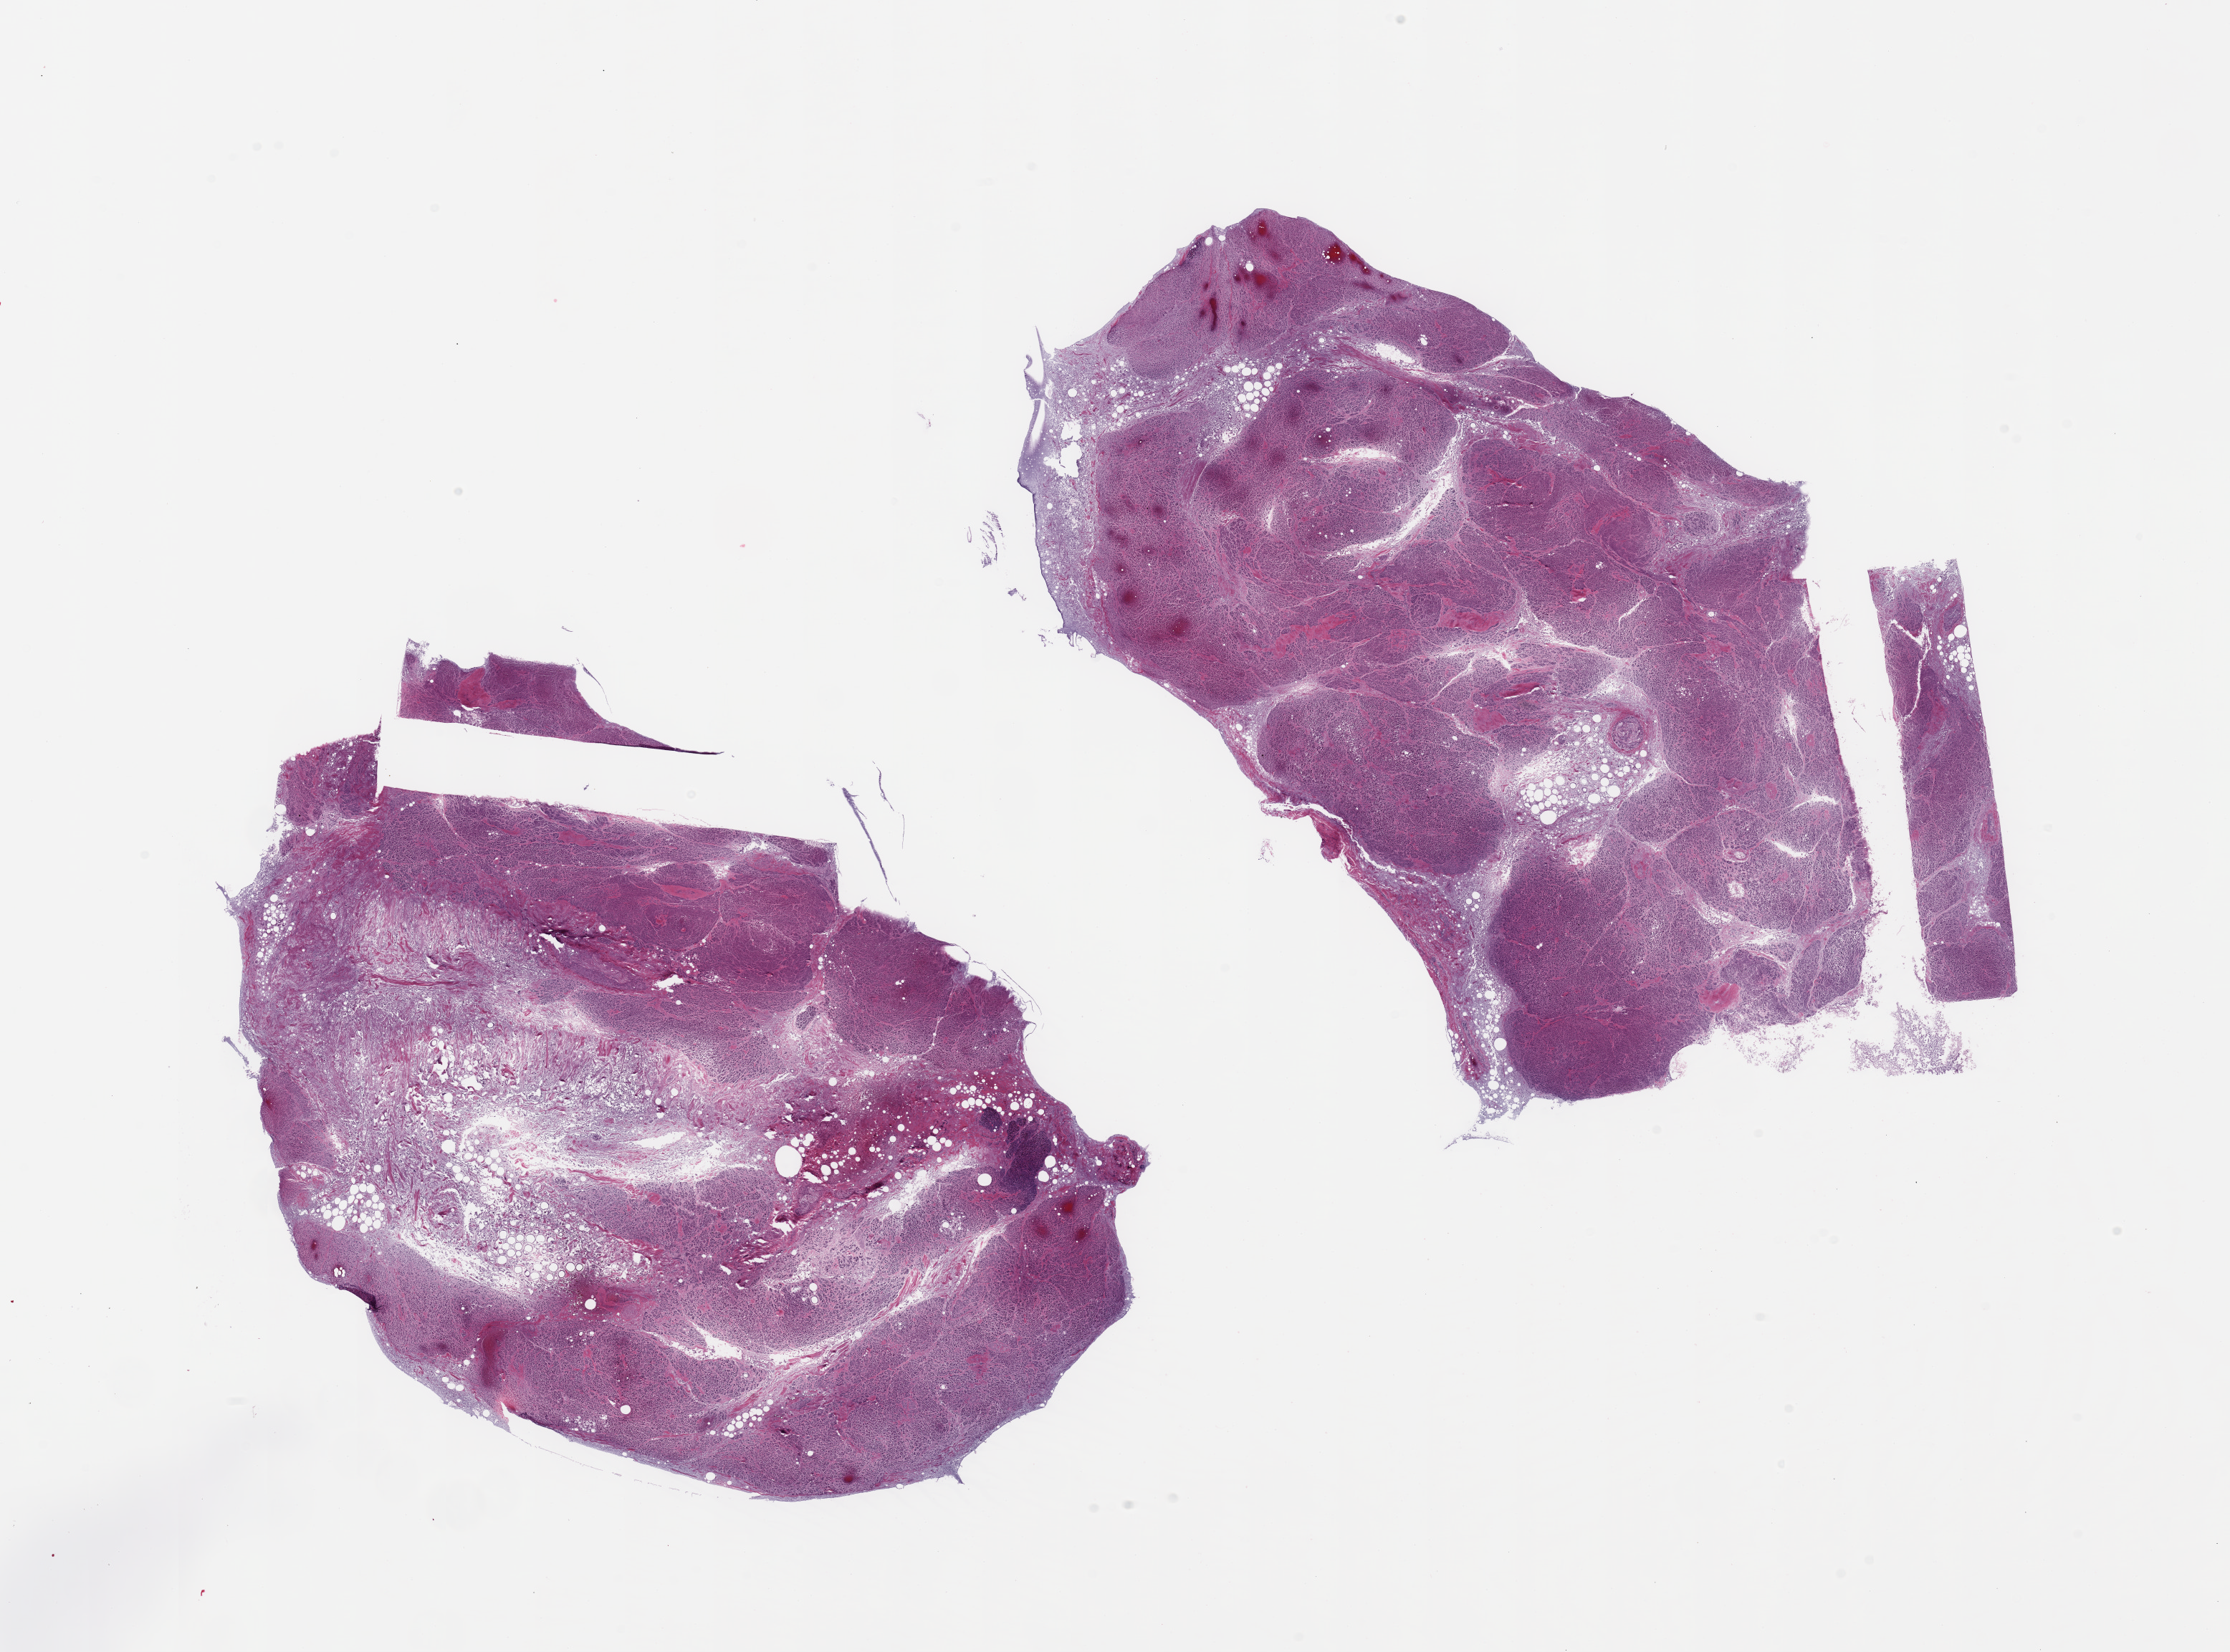
Digitized H&E-stained section — a low-resolution overview of the entire scanned area, about 24.6 x 18.2 mm (from a 20x scan), PAXgene-fixed paraffin-embedded (PFPE) section, section of pancreas (target tissue), donor tissue sample. Donor: female.
Review note (as recorded): 2 pieces, advanced saponfication; islets not visible.